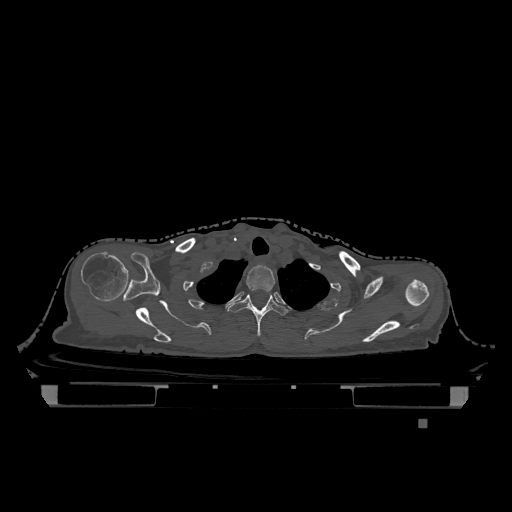
CT including the spine, one axial slice. Position 975 of 1317 along the scan axis. Bone window (W 1800 / L 400 HU). 0.5 mm slice thickness. 512 × 512 image matrix, field of view 500 × 500 mm. Female patient, age 74 years. From the clinical record (not read from this slice): primary cancer: lung.
Structures marked on this image (semi-automatic segmentation, software-assisted and operator-edited):
- T1 vertebra: bounding box <246,265,275,292> (left, top, right, bottom; pixels)
- T2 vertebra: <228,294,288,336>